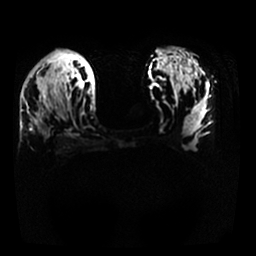
Breast MRI, one axial slice. Slice 19 of 25 in the series (ordered by position). Diffusion-weighted series; image 2 of 4 stored at this slice position (different b-values; order by instance number). 1.5 T. 4 mm slice thickness. 256 × 256 image matrix. Female patient.
Outlined on this slice (expert manual segmentation):
- tumour on diffusion-weighted imaging: box from (x=29, y=85) to (x=53, y=134) px